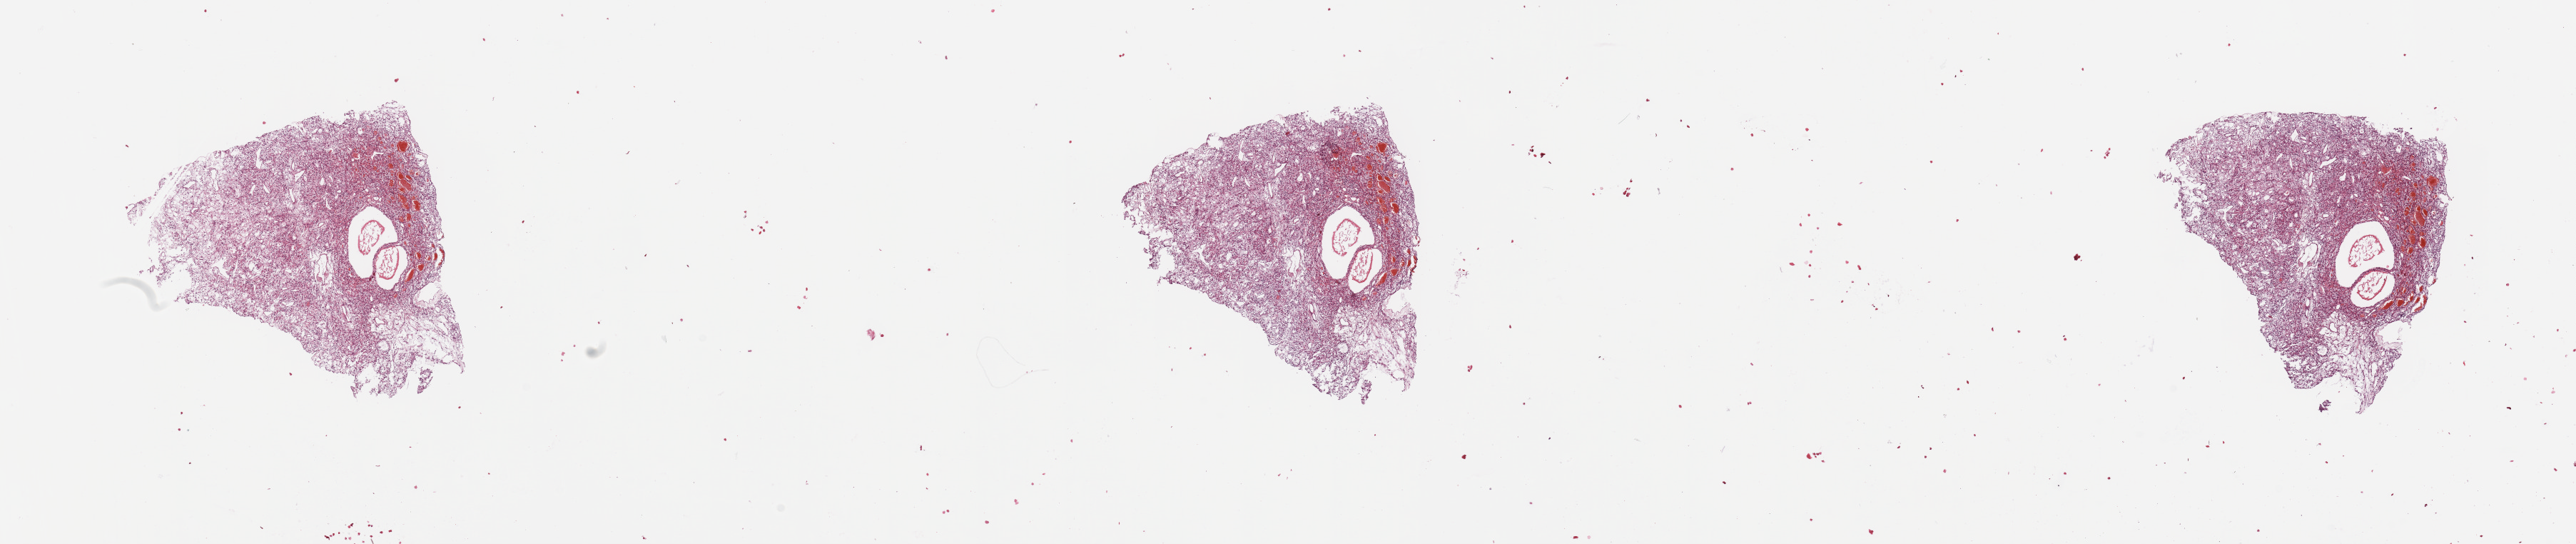
Digitized H&E tissue section (whole slide), low-resolution overview of the scanned area, about 28.5 x 6.0 mm, tumour tissue sample, kidney. Patient: male, age 72 years. Histologic grade: G2 (moderately differentiated).
AJCC pathologic stage: III. Diagnosis: Renal cell carcinoma, NOS. Primary tumour site (as recorded): middle.